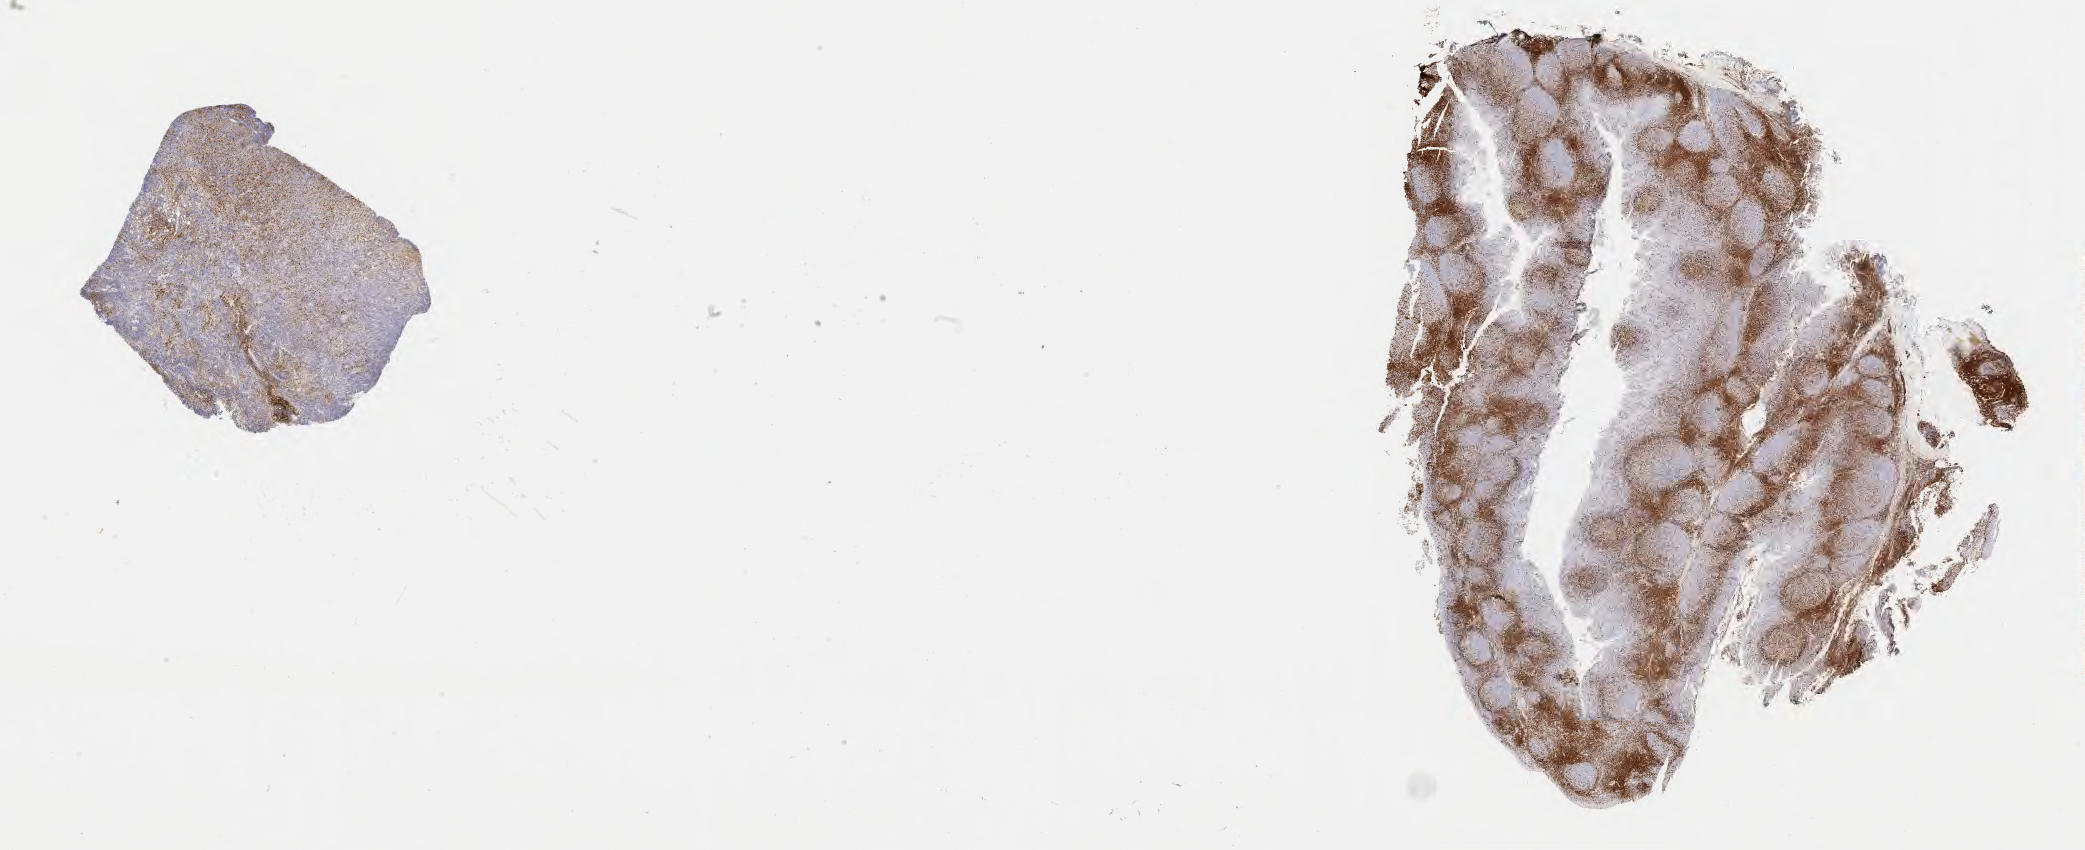
IHC for CD3, whole-slide image — whole scanned area (about 33.7 x 13.7 mm) shown as a low-resolution overview; tumor tissue; anatomic site: buccal mucosa. Male, age 7 years at initial diagnosis.
* histologic diagnosis: Burkitt lymphoma, NOS